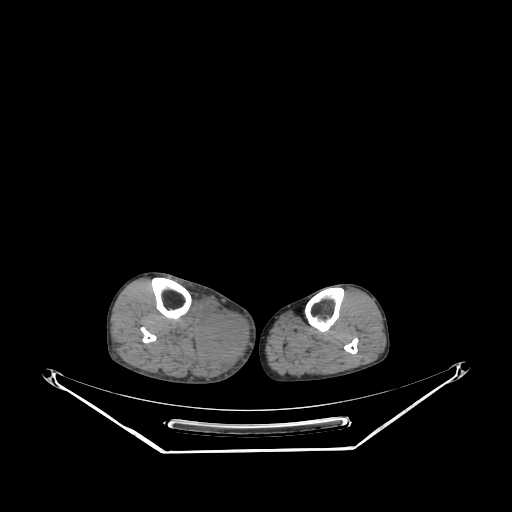
CT of an extremity soft-tissue mass (from a PET/CT study), one axial slice; position 141 of 267 along the scan axis; soft-tissue window (W 400 / L 40 HU); 512 × 512 image matrix. Male patient. Case-level facts recorded for this patient, not image findings: histological type: pleiomorphic liposarcoma; grade: high; site of the primary tumour: right calf.
Annotated regions visible in this slice (expert contour drawn on MRI and transferred to this co-registered scan by the dataset authors):
- gross tumour volume including surrounding oedema: bounding box (x1, y1, x2, y2) in pixels: (198, 306, 248, 366)
- gross tumour volume (mass): (201, 313, 248, 362)